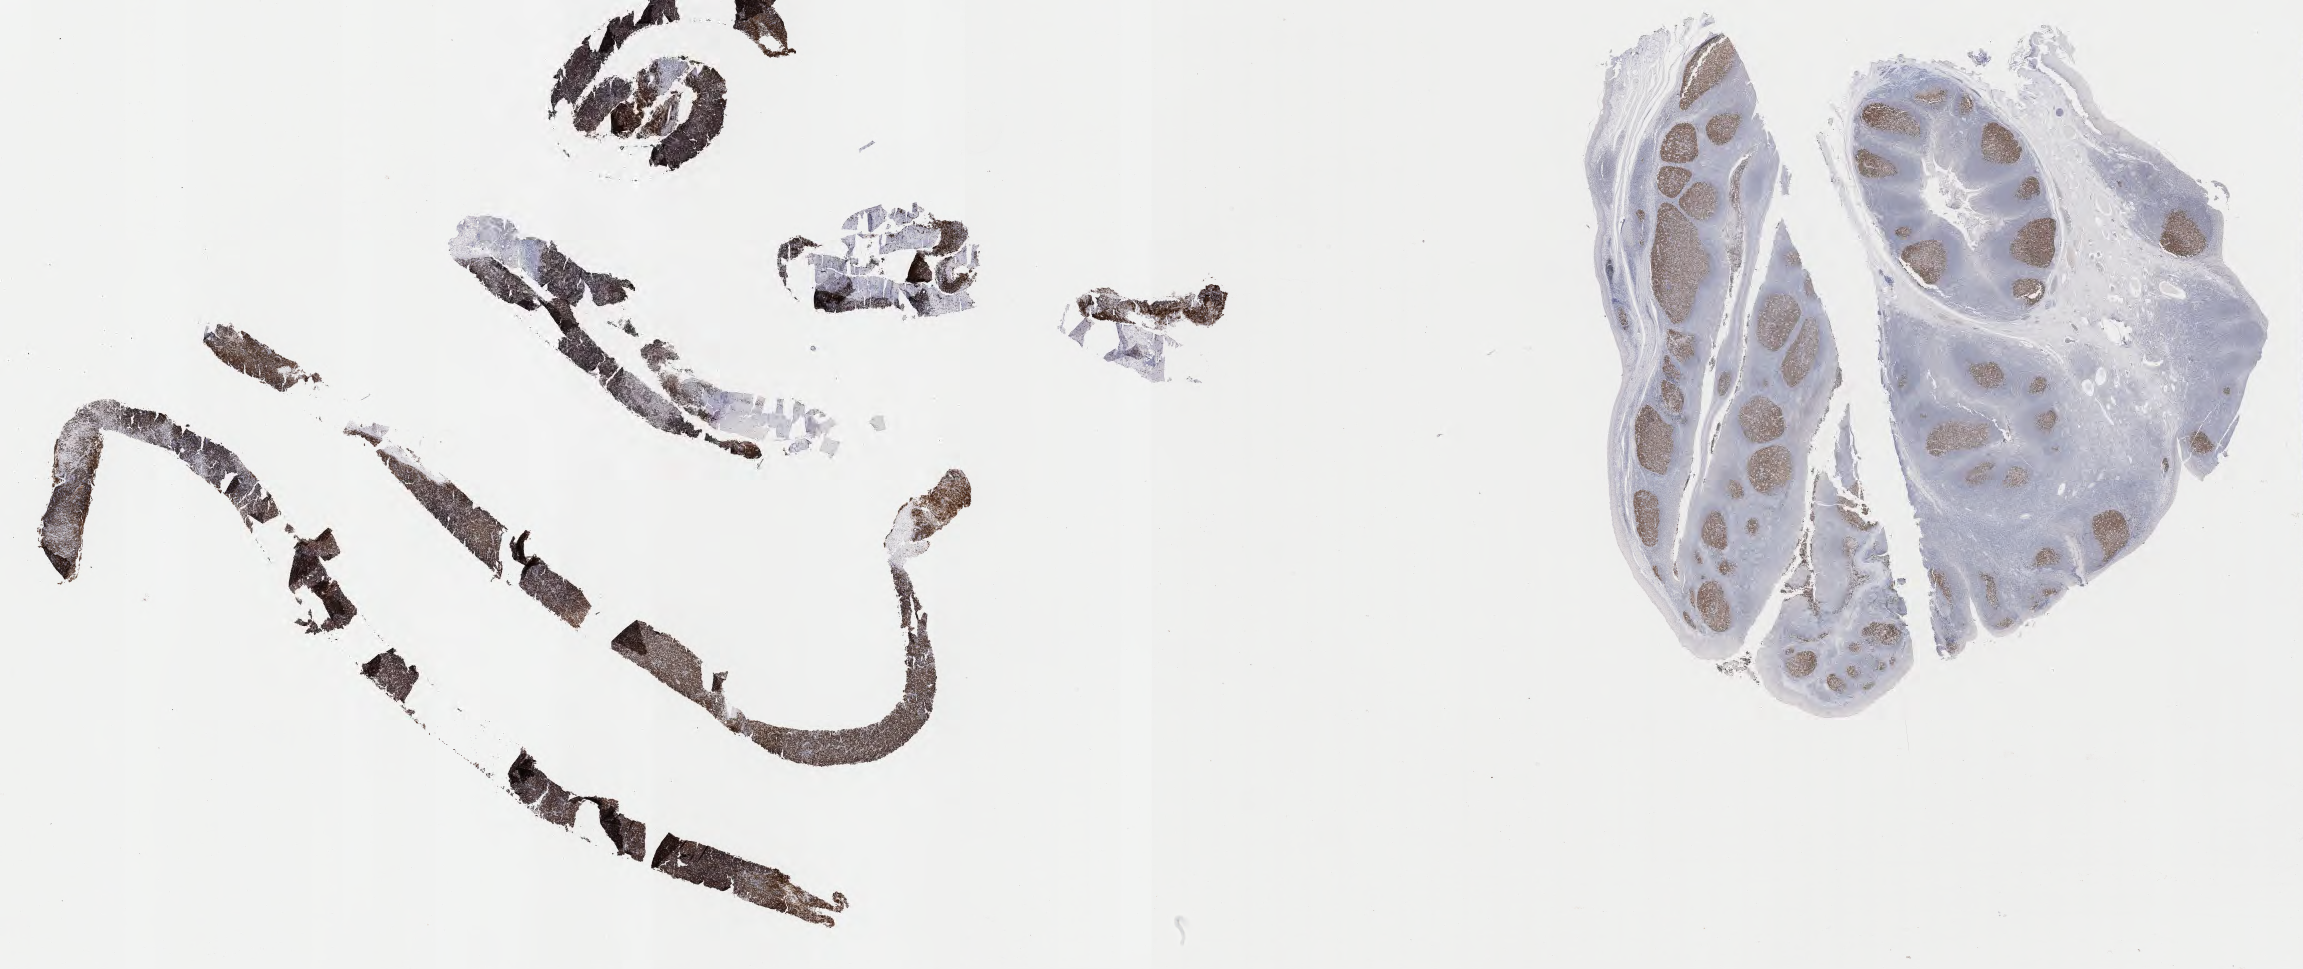
Whole-slide image, immunohistochemical stain for BCL6 — shown as a low-resolution overview of the whole scanned area (about 37.2 x 15.7 mm). Tumor tissue. Male patient, 45 years old.
* diagnosis: Burkitt lymphoma, NOS